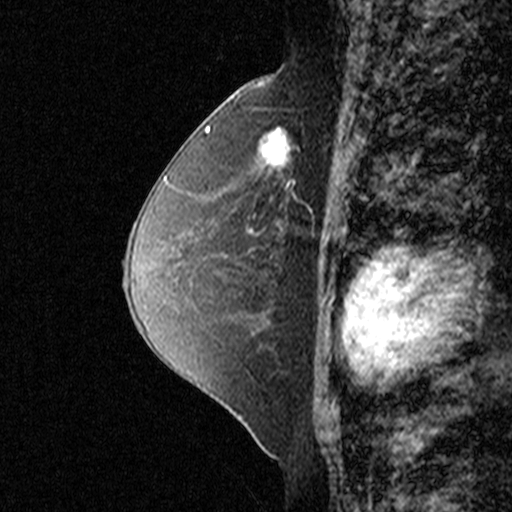
Breast MRI (dynamic contrast-enhanced), one sagittal slice. Position 23 of 44 along the scan axis. Dynamic contrast-enhanced study with each time point stored as its own series, time point 2 of 3 at this slice position (early post-contrast, ordered by acquisition time). 1.5 T. TE 4.5 ms, TR 11 ms. 512 × 512 image matrix, field of view 200 × 200 mm. Female patient, age 49 years. From the clinical record (not read from this slice): setting: breast cancer imaged before/during neoadjuvant chemotherapy; receptor status: triple-negative.
Structures marked on this image (semi-automatic segmentation, software-assisted and operator-edited):
- analysis volume of interest (the breast-tissue region the enhancement analysis was run in; not a lesion): bounding box (x1, y1, x2, y2) in pixels: (236, 100, 335, 197)
- tumour enhancement mask (voxels above the 90 % enhancement threshold inside the analysis volume of interest): (263, 127, 300, 187)